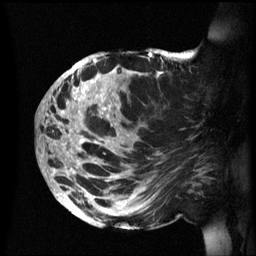
Breast MRI (dynamic contrast-enhanced), one sagittal slice; dynamic contrast-enhanced series, image 2 of 3 at this slice position (ordered by acquisition); 1.5 T; TE 4.2 ms, TR 8.4 ms; 2.4 mm slice thickness; 256 × 256 image matrix, field of view 230 × 230 mm. Female patient, age 48 years.
Structures marked on this image (semi-automatically segmented with operator editing):
- analysis volume of interest (the breast-tissue region the enhancement analysis was run in; not a lesion): bounding box [x1, y1, x2, y2] px = [42, 49, 202, 230]
- tumour enhancement mask (voxels above the 70 % enhancement threshold inside the analysis volume of interest): [42, 52, 163, 224]